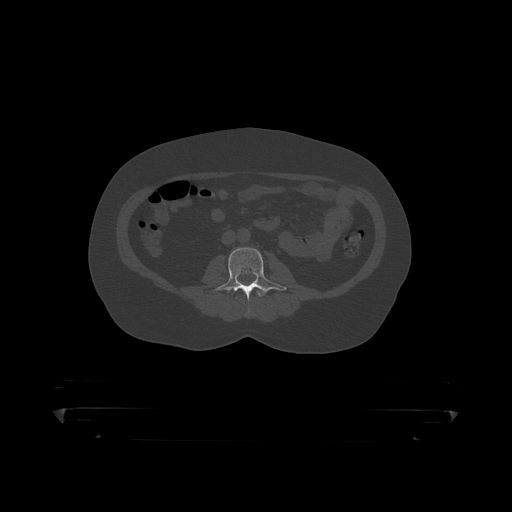
CT including the spine, one axial slice. Slice 92 of 390 in the series (ordered by position). Bone window (W 1800 / L 400 HU). 1.25 mm slice thickness. 512 × 512 image matrix. Patient: male, 60 years. Case-level facts recorded for this patient, not image findings: primary cancer: prostate.
Annotated regions visible in this slice (semi-automatic segmentation, software-assisted and operator-edited):
- L2 vertebra: bounding box [x1, y1, x2, y2] px = [237, 291, 263, 315]
- L3 vertebra: [211, 248, 286, 299]